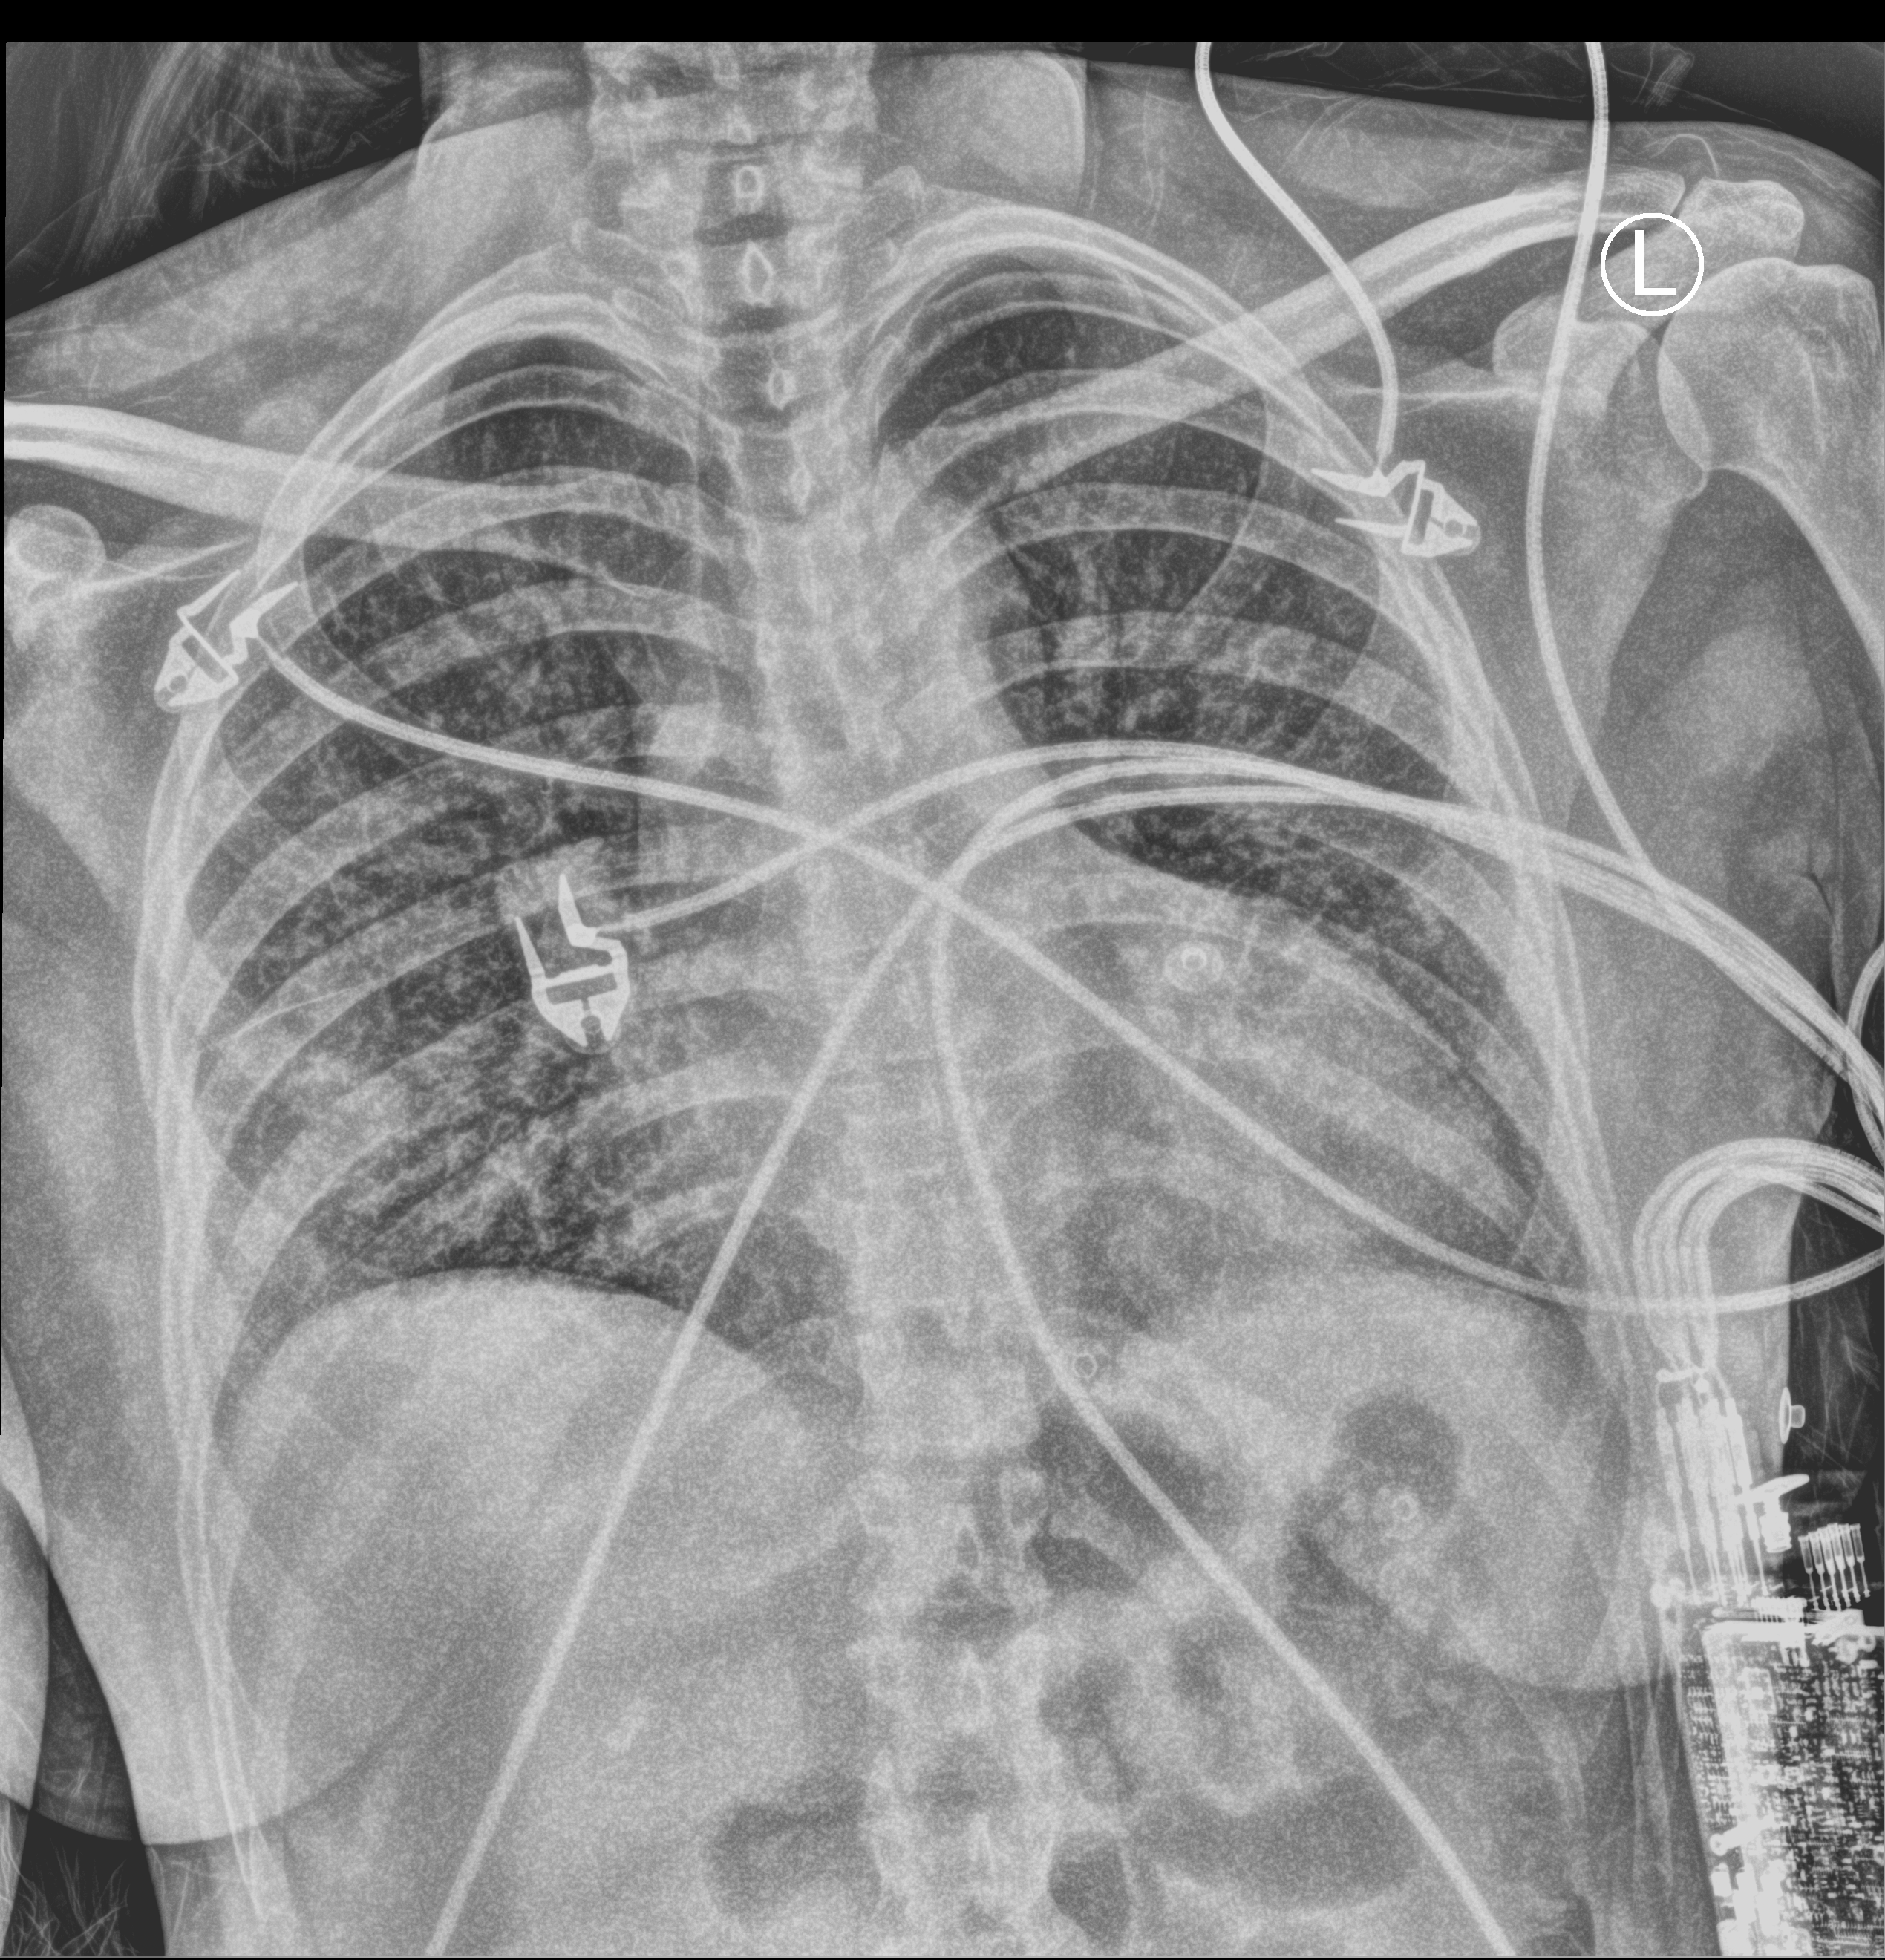
Portable chest radiograph, anteroposterior (AP) projection. Patient hospitalised with COVID-19; female, aged 18–59 years.
Hospital-stay facts (about this admission, not read from this image; timing relative to this image not recorded): admitted to intensive care during this hospital stay: no; mechanically ventilated during this hospital stay: no.